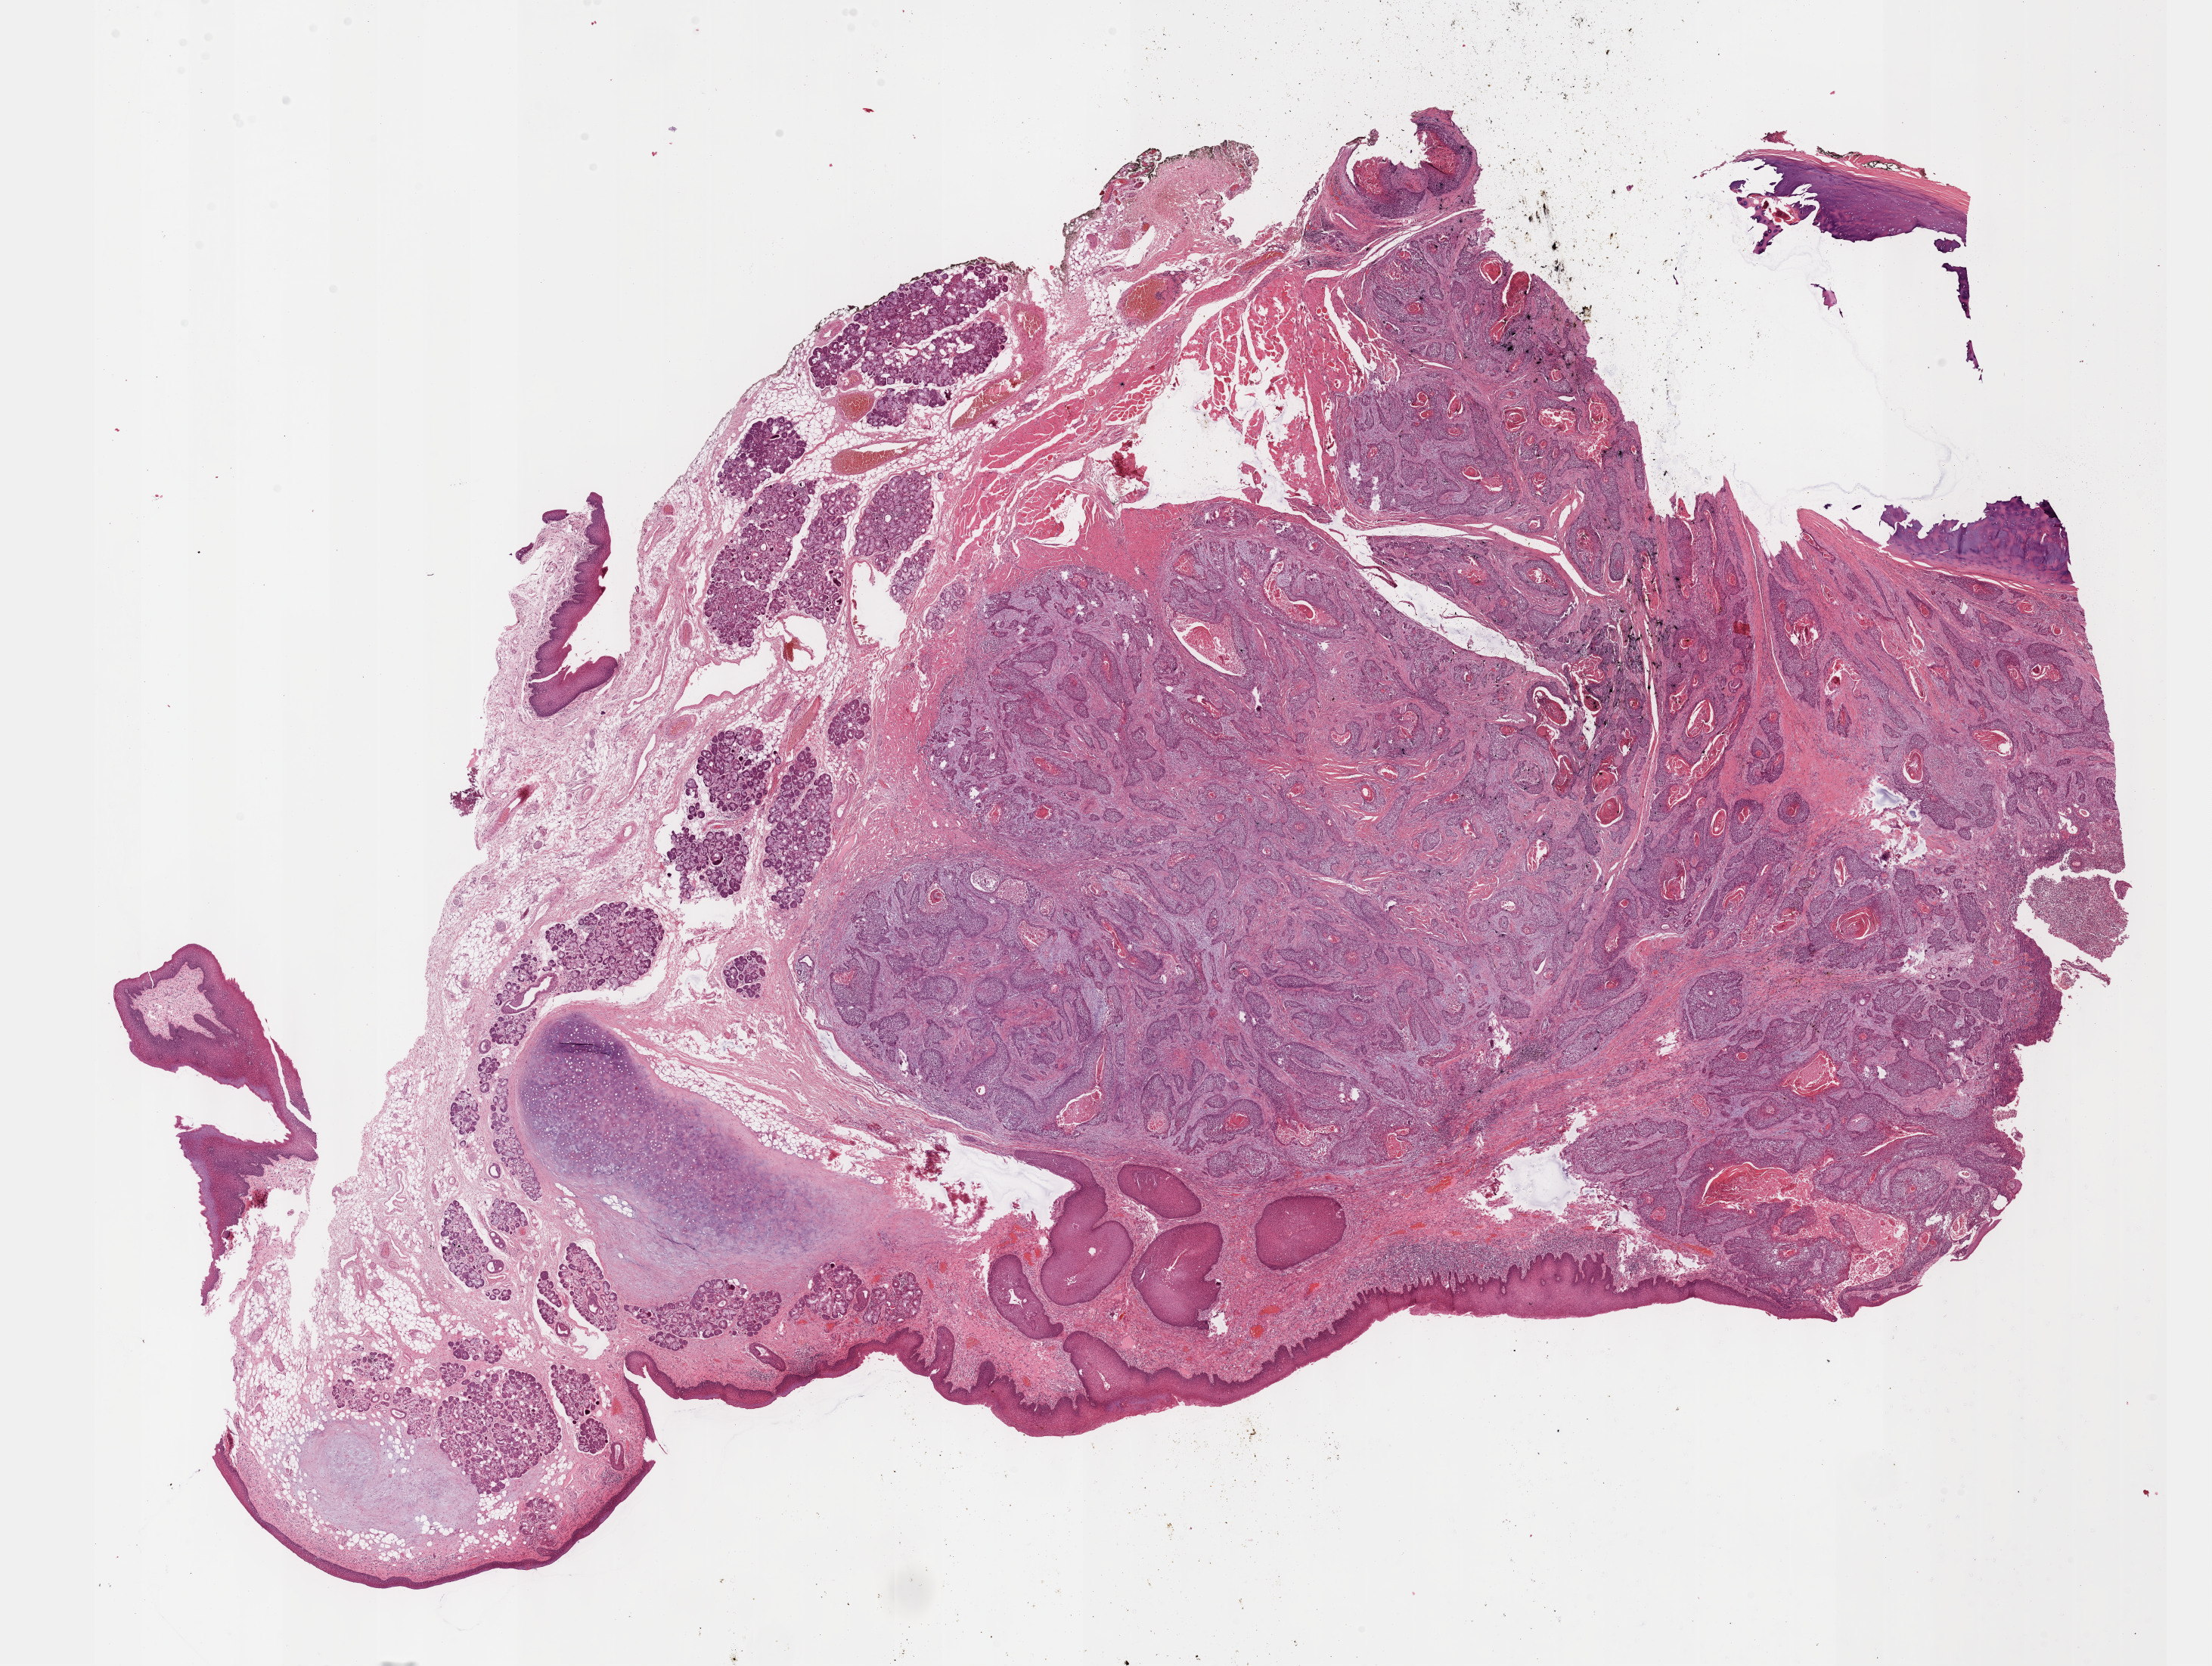
Whole-slide histology image, Hematoxylin and eosin (H&E) stained — a low-resolution overview of the entire scanned area, about 23.6 x 17.8 mm; formalin-fixed paraffin-embedded (FFPE) diagnostic section; head and neck, primary tumour sample. Patient: male, age at initial diagnosis 75 years. Histologic grade: G2 (moderately differentiated).
* AJCC pathologic stage: IVA
* lymph nodes positive (case pathology): 0 of 18 examined
* diagnosis: Squamous cell carcinoma, NOS
* laterality: right